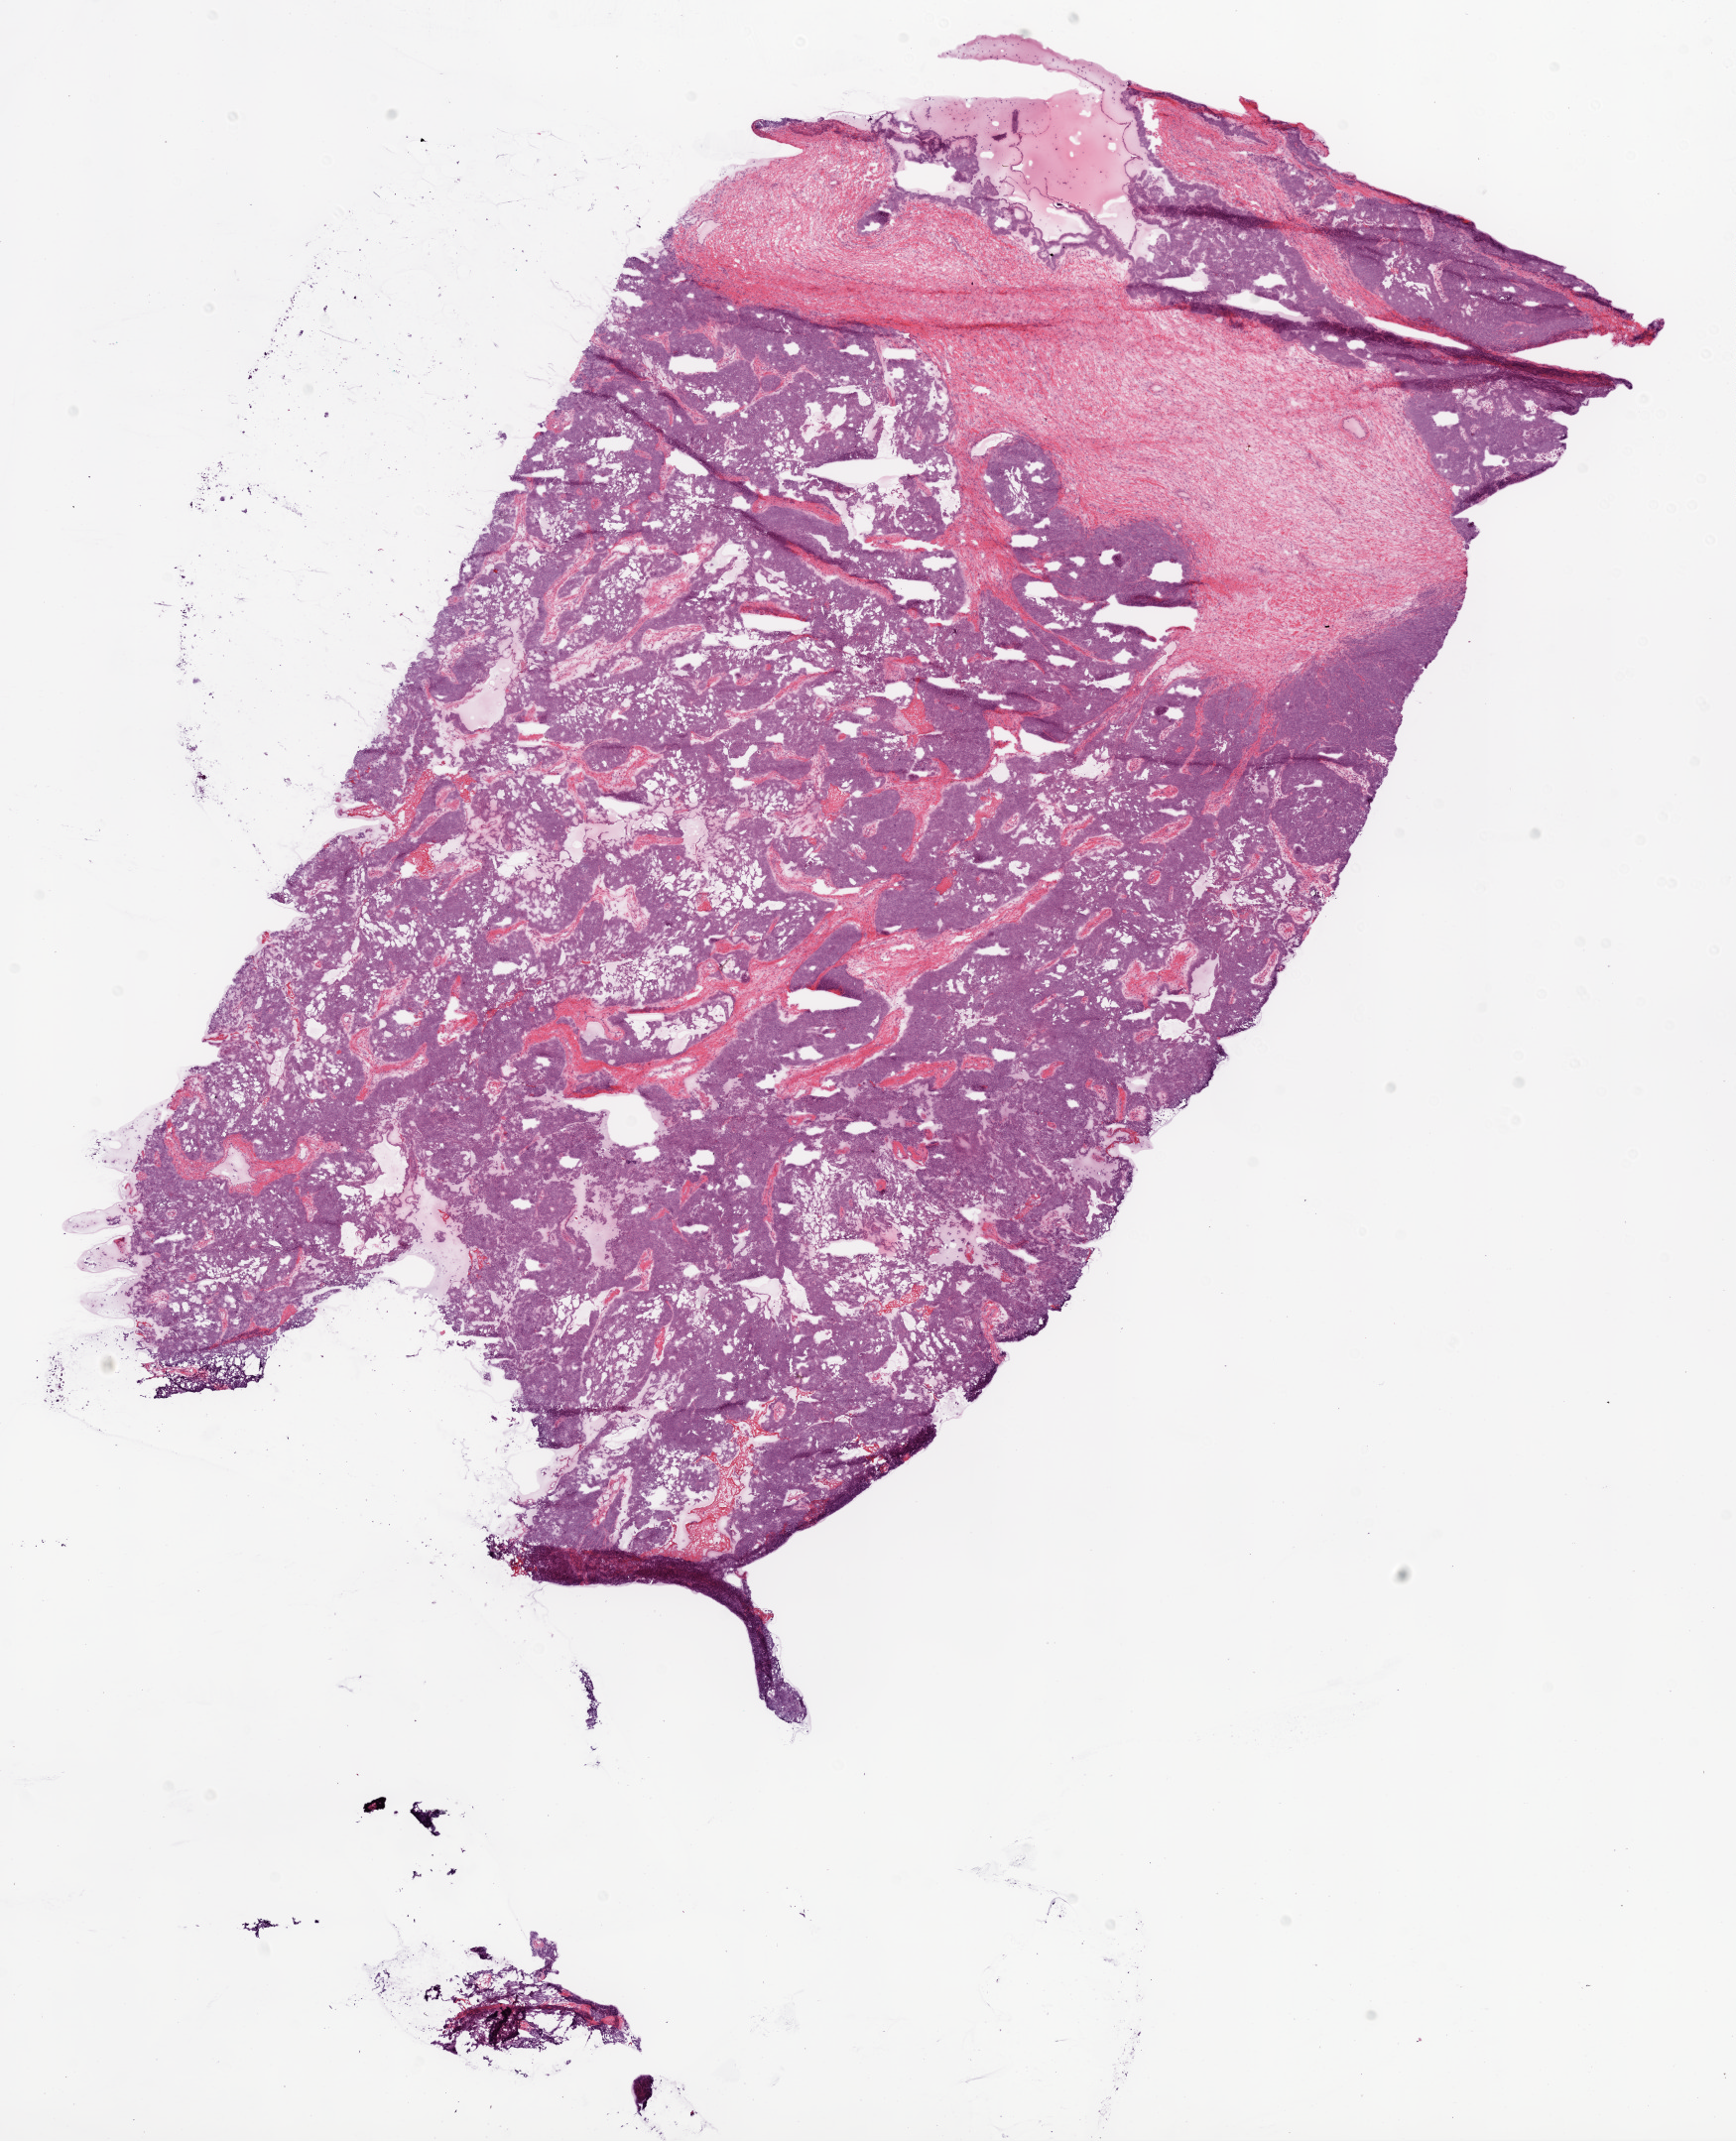
Digitized H&E-stained tissue section (whole slide), whole scanned area (about 14.0 x 17.3 mm, acquisition: 20x scan) shown as a low-resolution overview; frozen section from the bottom of the tissue portion; sample: primary tumour, ovary. Female, age 83 years at initial diagnosis. Histologic grade: G3 (poorly differentiated). Slide review estimates, as recorded: tumour cells 80%, tumour nuclei 95%, normal cells 15%, stromal cells 5%, necrosis 5%.
FIGO stage: IIIB. Pathologic diagnosis: Serous cystadenocarcinoma, NOS.